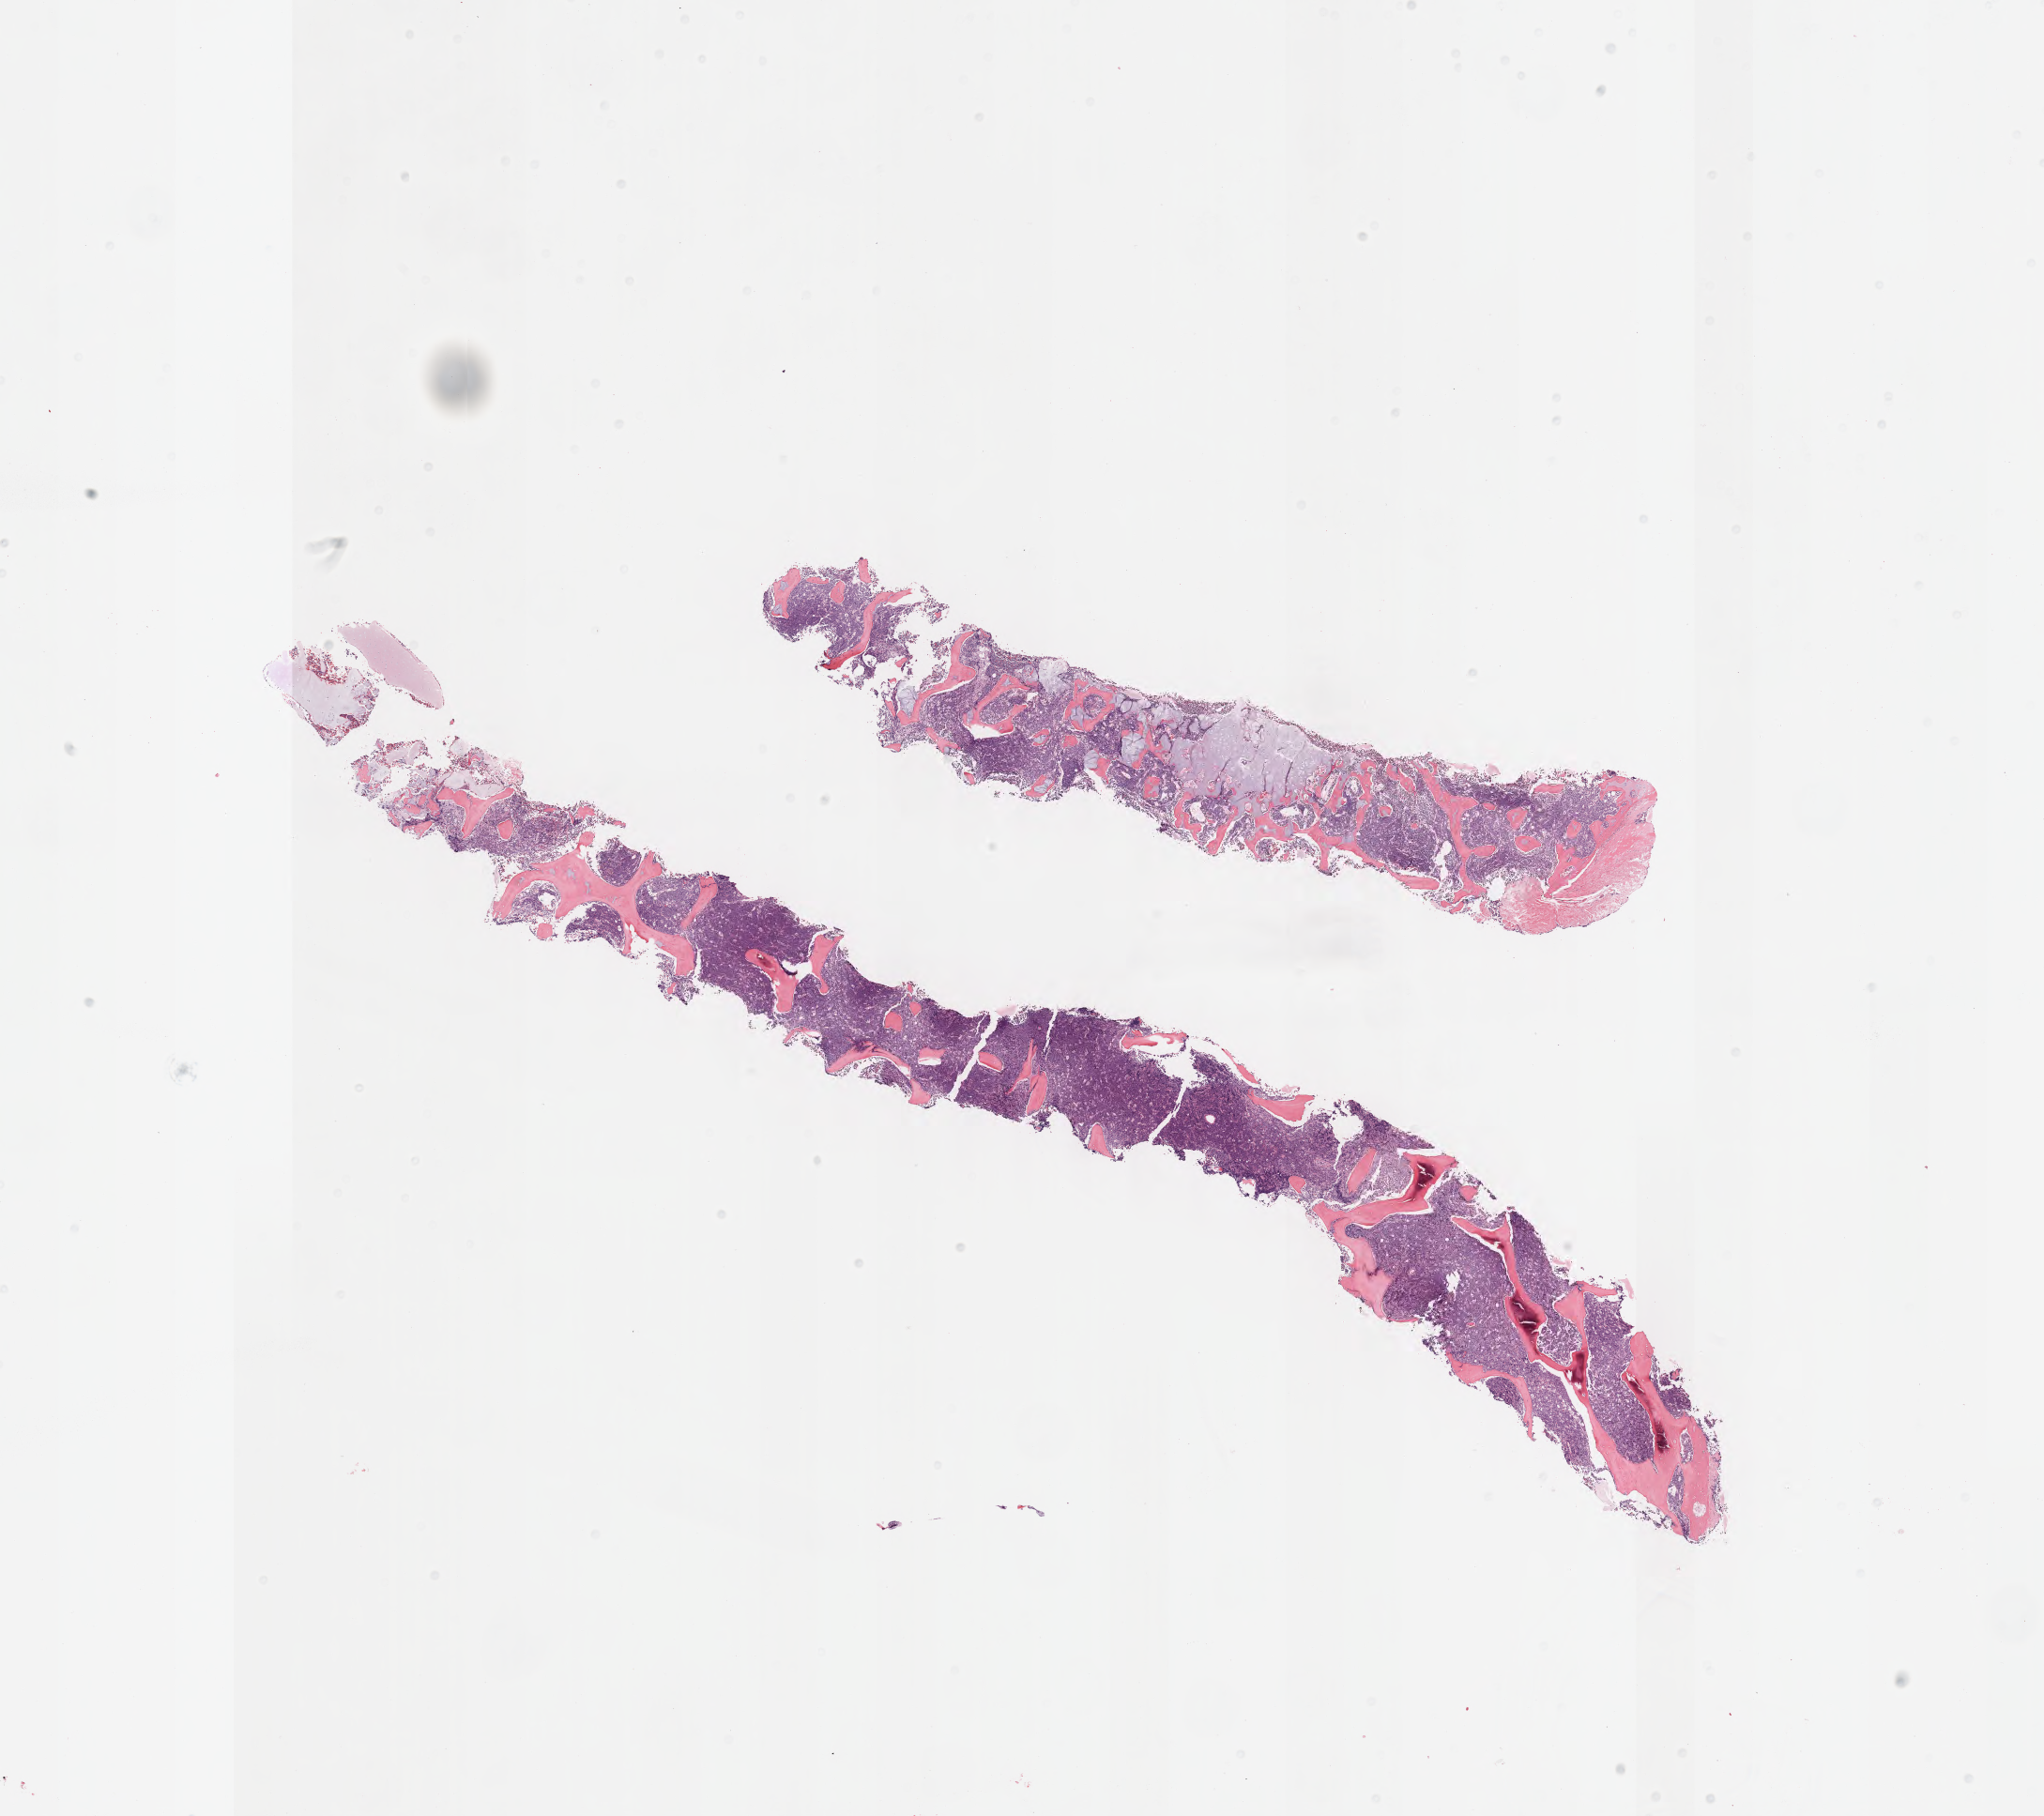
Whole-slide image, hematoxylin and eosin (H&E) stain, low-resolution overview of the scanned area, about 17.6 x 15.6 mm. Specimen: tumor tissue. Anatomic site: bone marrow. Patient male; age 11 years.
• diagnosis: Burkitt lymphoma, NOS